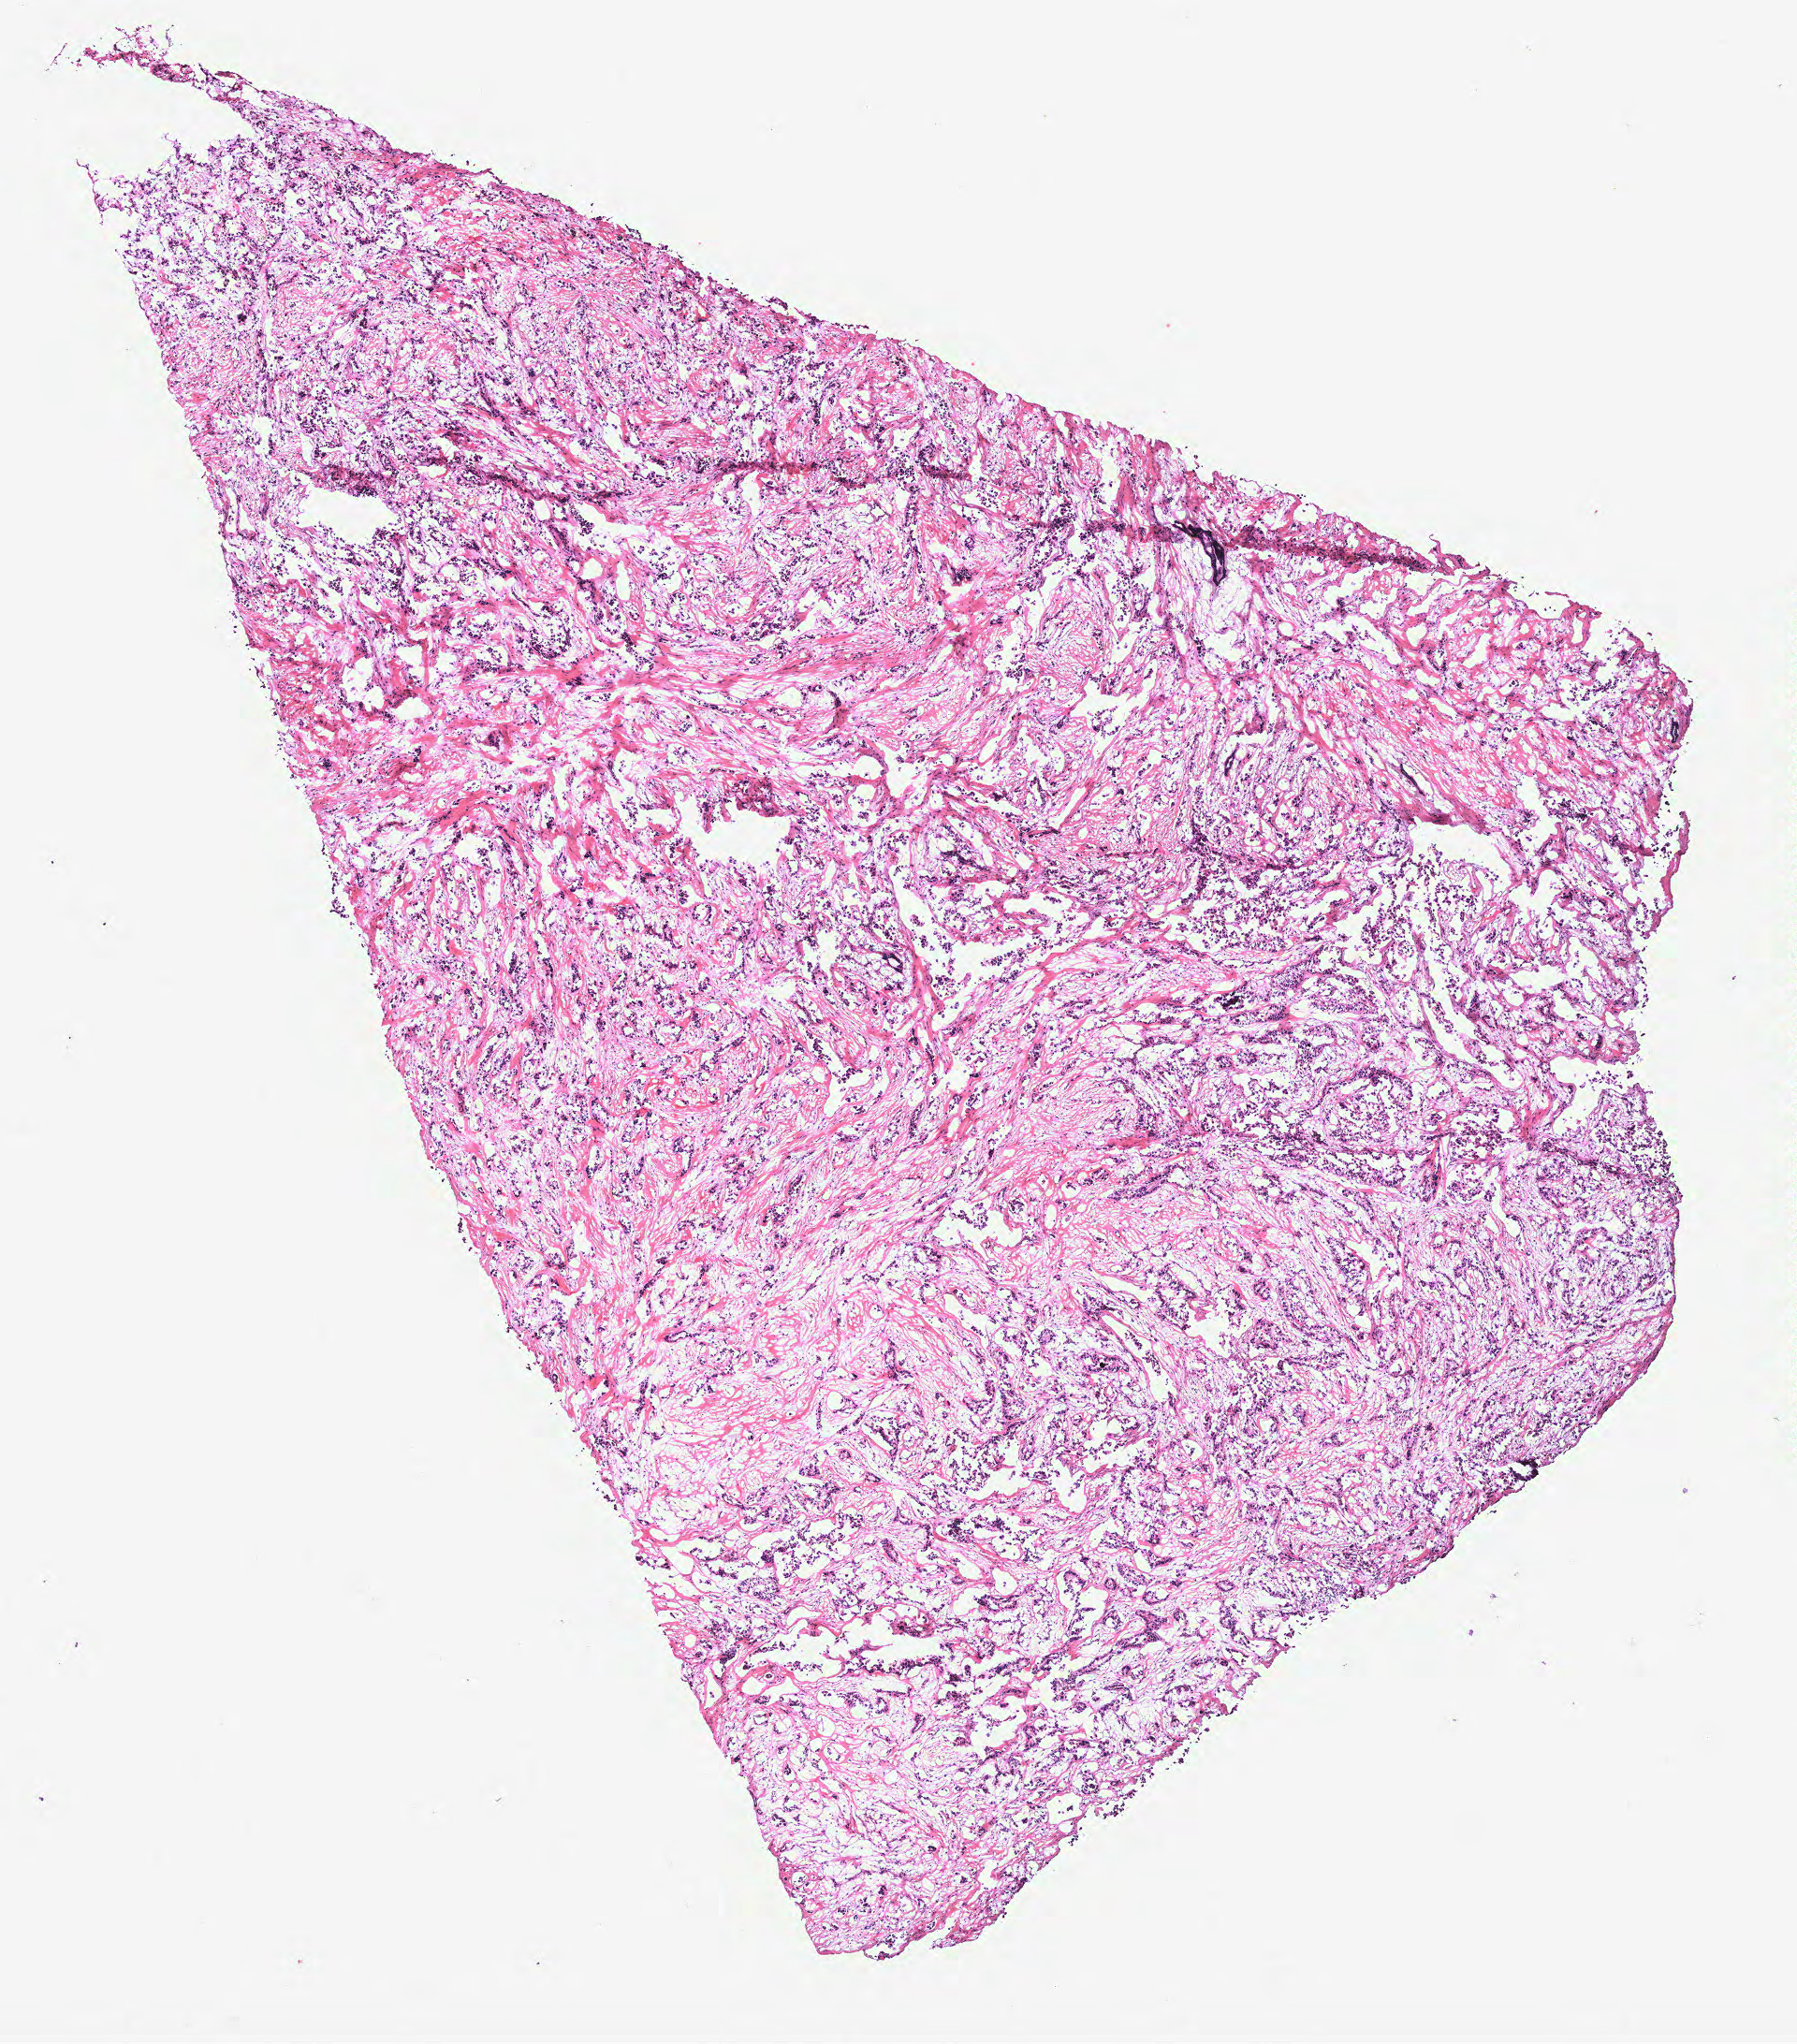
Digitized H&E-stained tissue section (whole slide) — a low-resolution overview of the entire scanned area, about 7.7 x 8.7 mm (from a 40x scan); tumour tissue sample, breast. 71-year-old female patient.
AJCC pathologic stage: IIA. Histologic diagnosis: Infiltrating duct carcinoma, NOS.